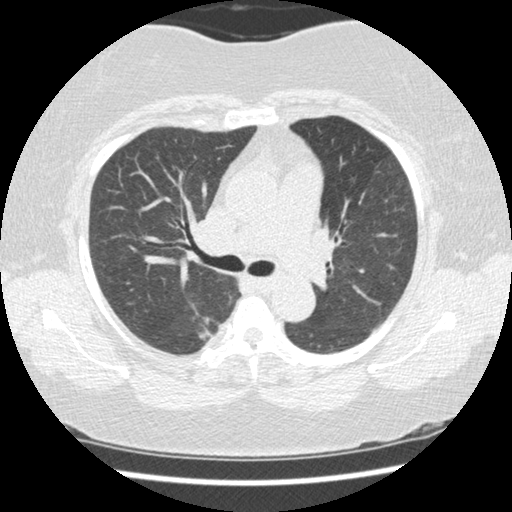
Chest CT (low-dose screening protocol), one axial image; second screening round (one year after baseline); lung window (W 1500 / L -600 HU); 1.25 mm slice thickness; standard (soft-tissue) reconstruction kernel (STANDARD); slice 66 of 210 in the series. Female, age 58 years at enrolment. Current smoker at enrolment.
Expert reader's lesion annotation, bounding box [x1, y1, x2, y2] px = [188, 307, 230, 359]. The exam's reader record, not a measurement of the box and not confirmed to be the same lesion: non-calcified nodule or mass ≥4 mm, right lower lobe, 15 × 15 mm, spiculated (stellate) margins, soft tissue attenuation, pre-existing on the prior screen: yes; interval growth: yes. Later outcome: lung cancer diagnosed 21 days after this screen — adenocarcinoma, NOS, right lower lobe, stage IB (AJCC 6th edition), 15 mm at pathology.